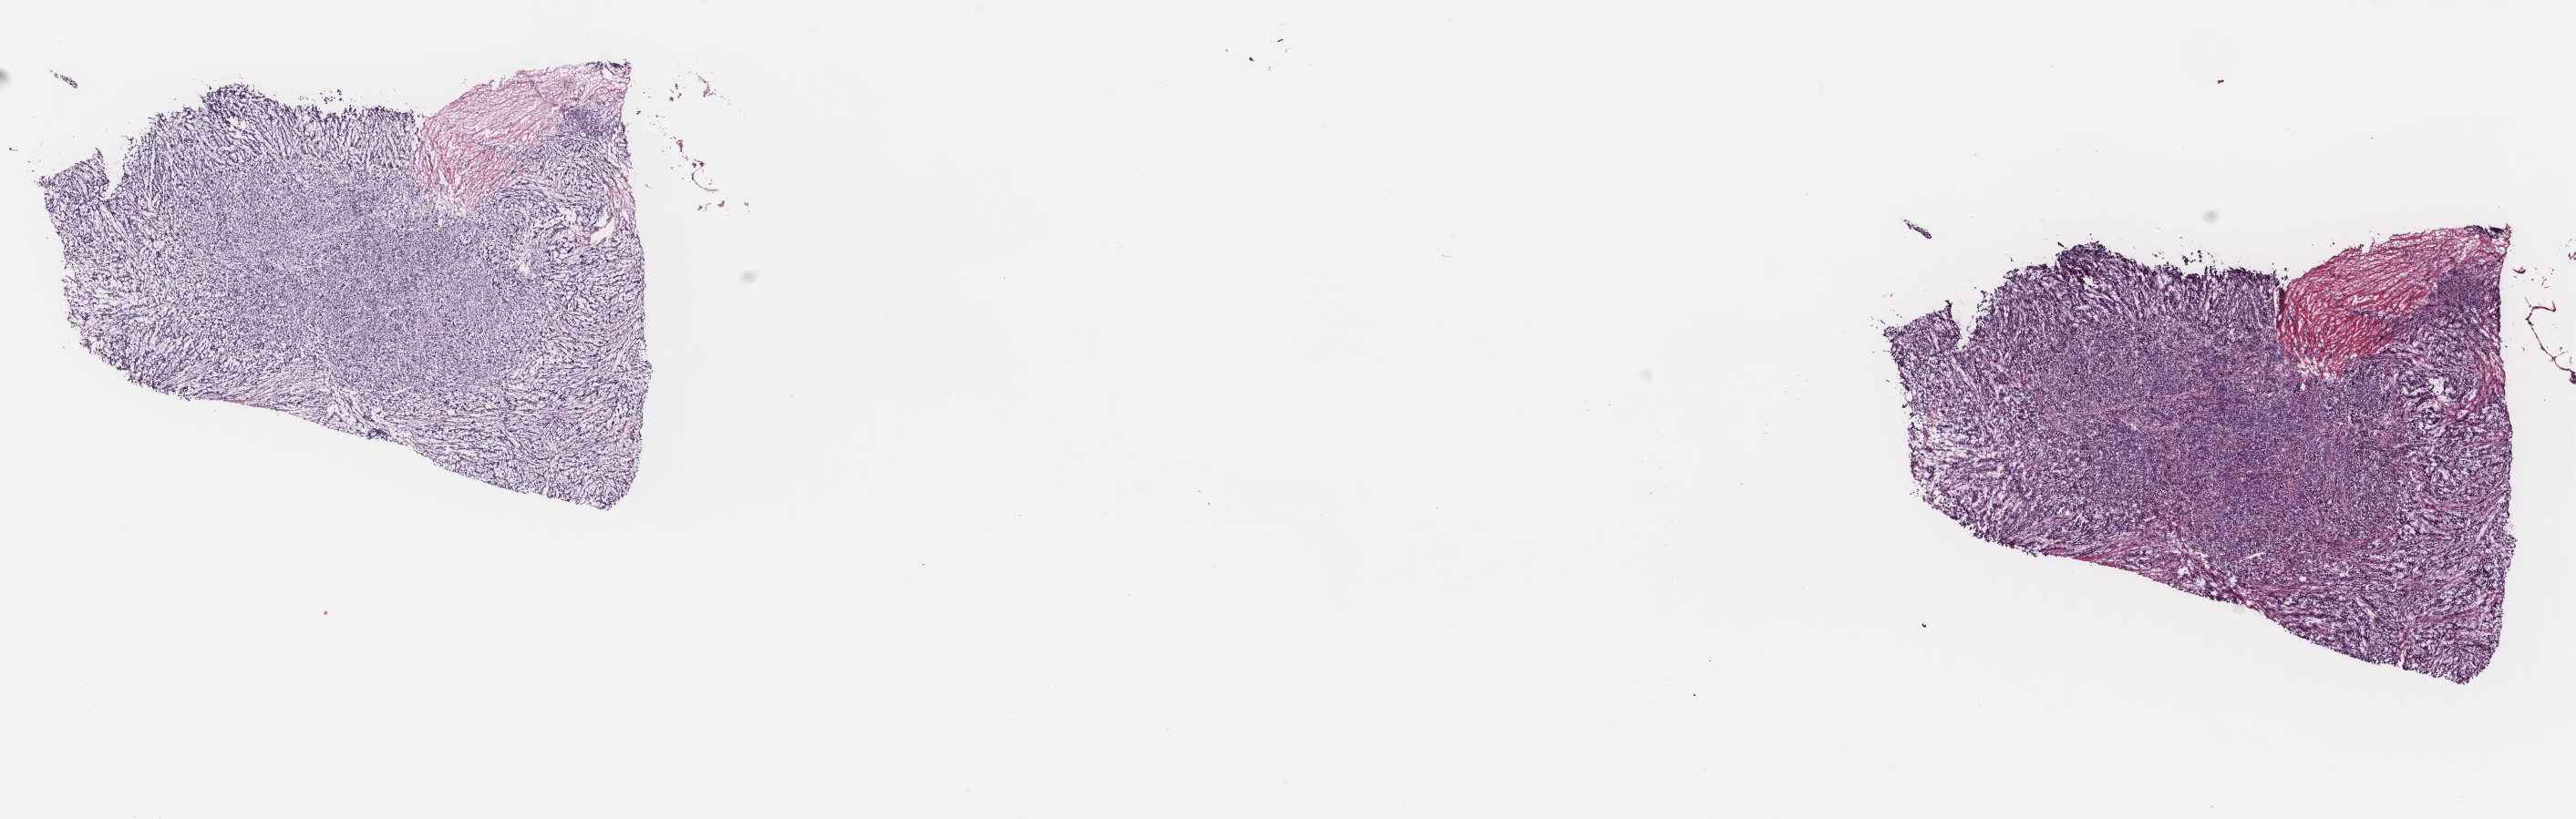
Whole-slide histology image, H&E, a low-resolution overview of the entire scanned area, about 22.4 x 7.1 mm (slide scanned at 40x), frozen section from the top of the tissue portion, metastatic tumour sample, sampled site: lymph nodes of axilla or arm. Male patient; age at initial diagnosis 34 years. Slide review estimates, as recorded: tumour cells 85%, tumour nuclei 85%, normal cells 0%, stromal cells 14%, necrosis 1%. Inflammatory infiltration, as recorded: lymphocyte infiltration 3%, monocyte infiltration 1%, neutrophil infiltration 1%.
* this section: metastatic tumour tissue
* patient diagnosis: Malignant melanoma, NOS